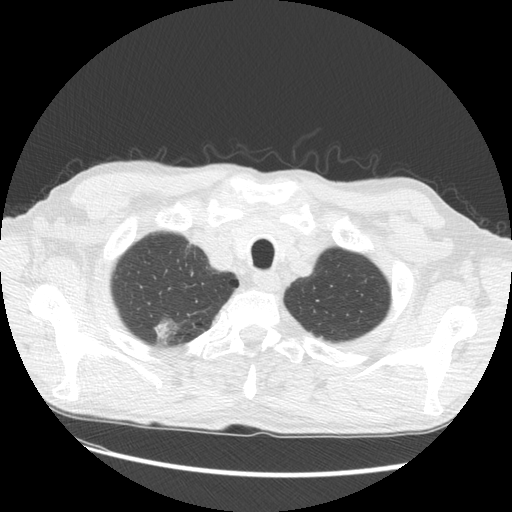
Low-dose screening chest CT, one axial slice. Position 121 of 133 along the scan axis. 120 kVp. Lung window (W 1500 / L -600 HU). 512 × 512 image matrix, field of view 360 × 360 mm.
Structures marked on this image (manually delineated by an expert):
- lesion 2 (tumor, upper lobe of right lung): bounding box <154,318,178,346> (left, top, right, bottom; pixels)